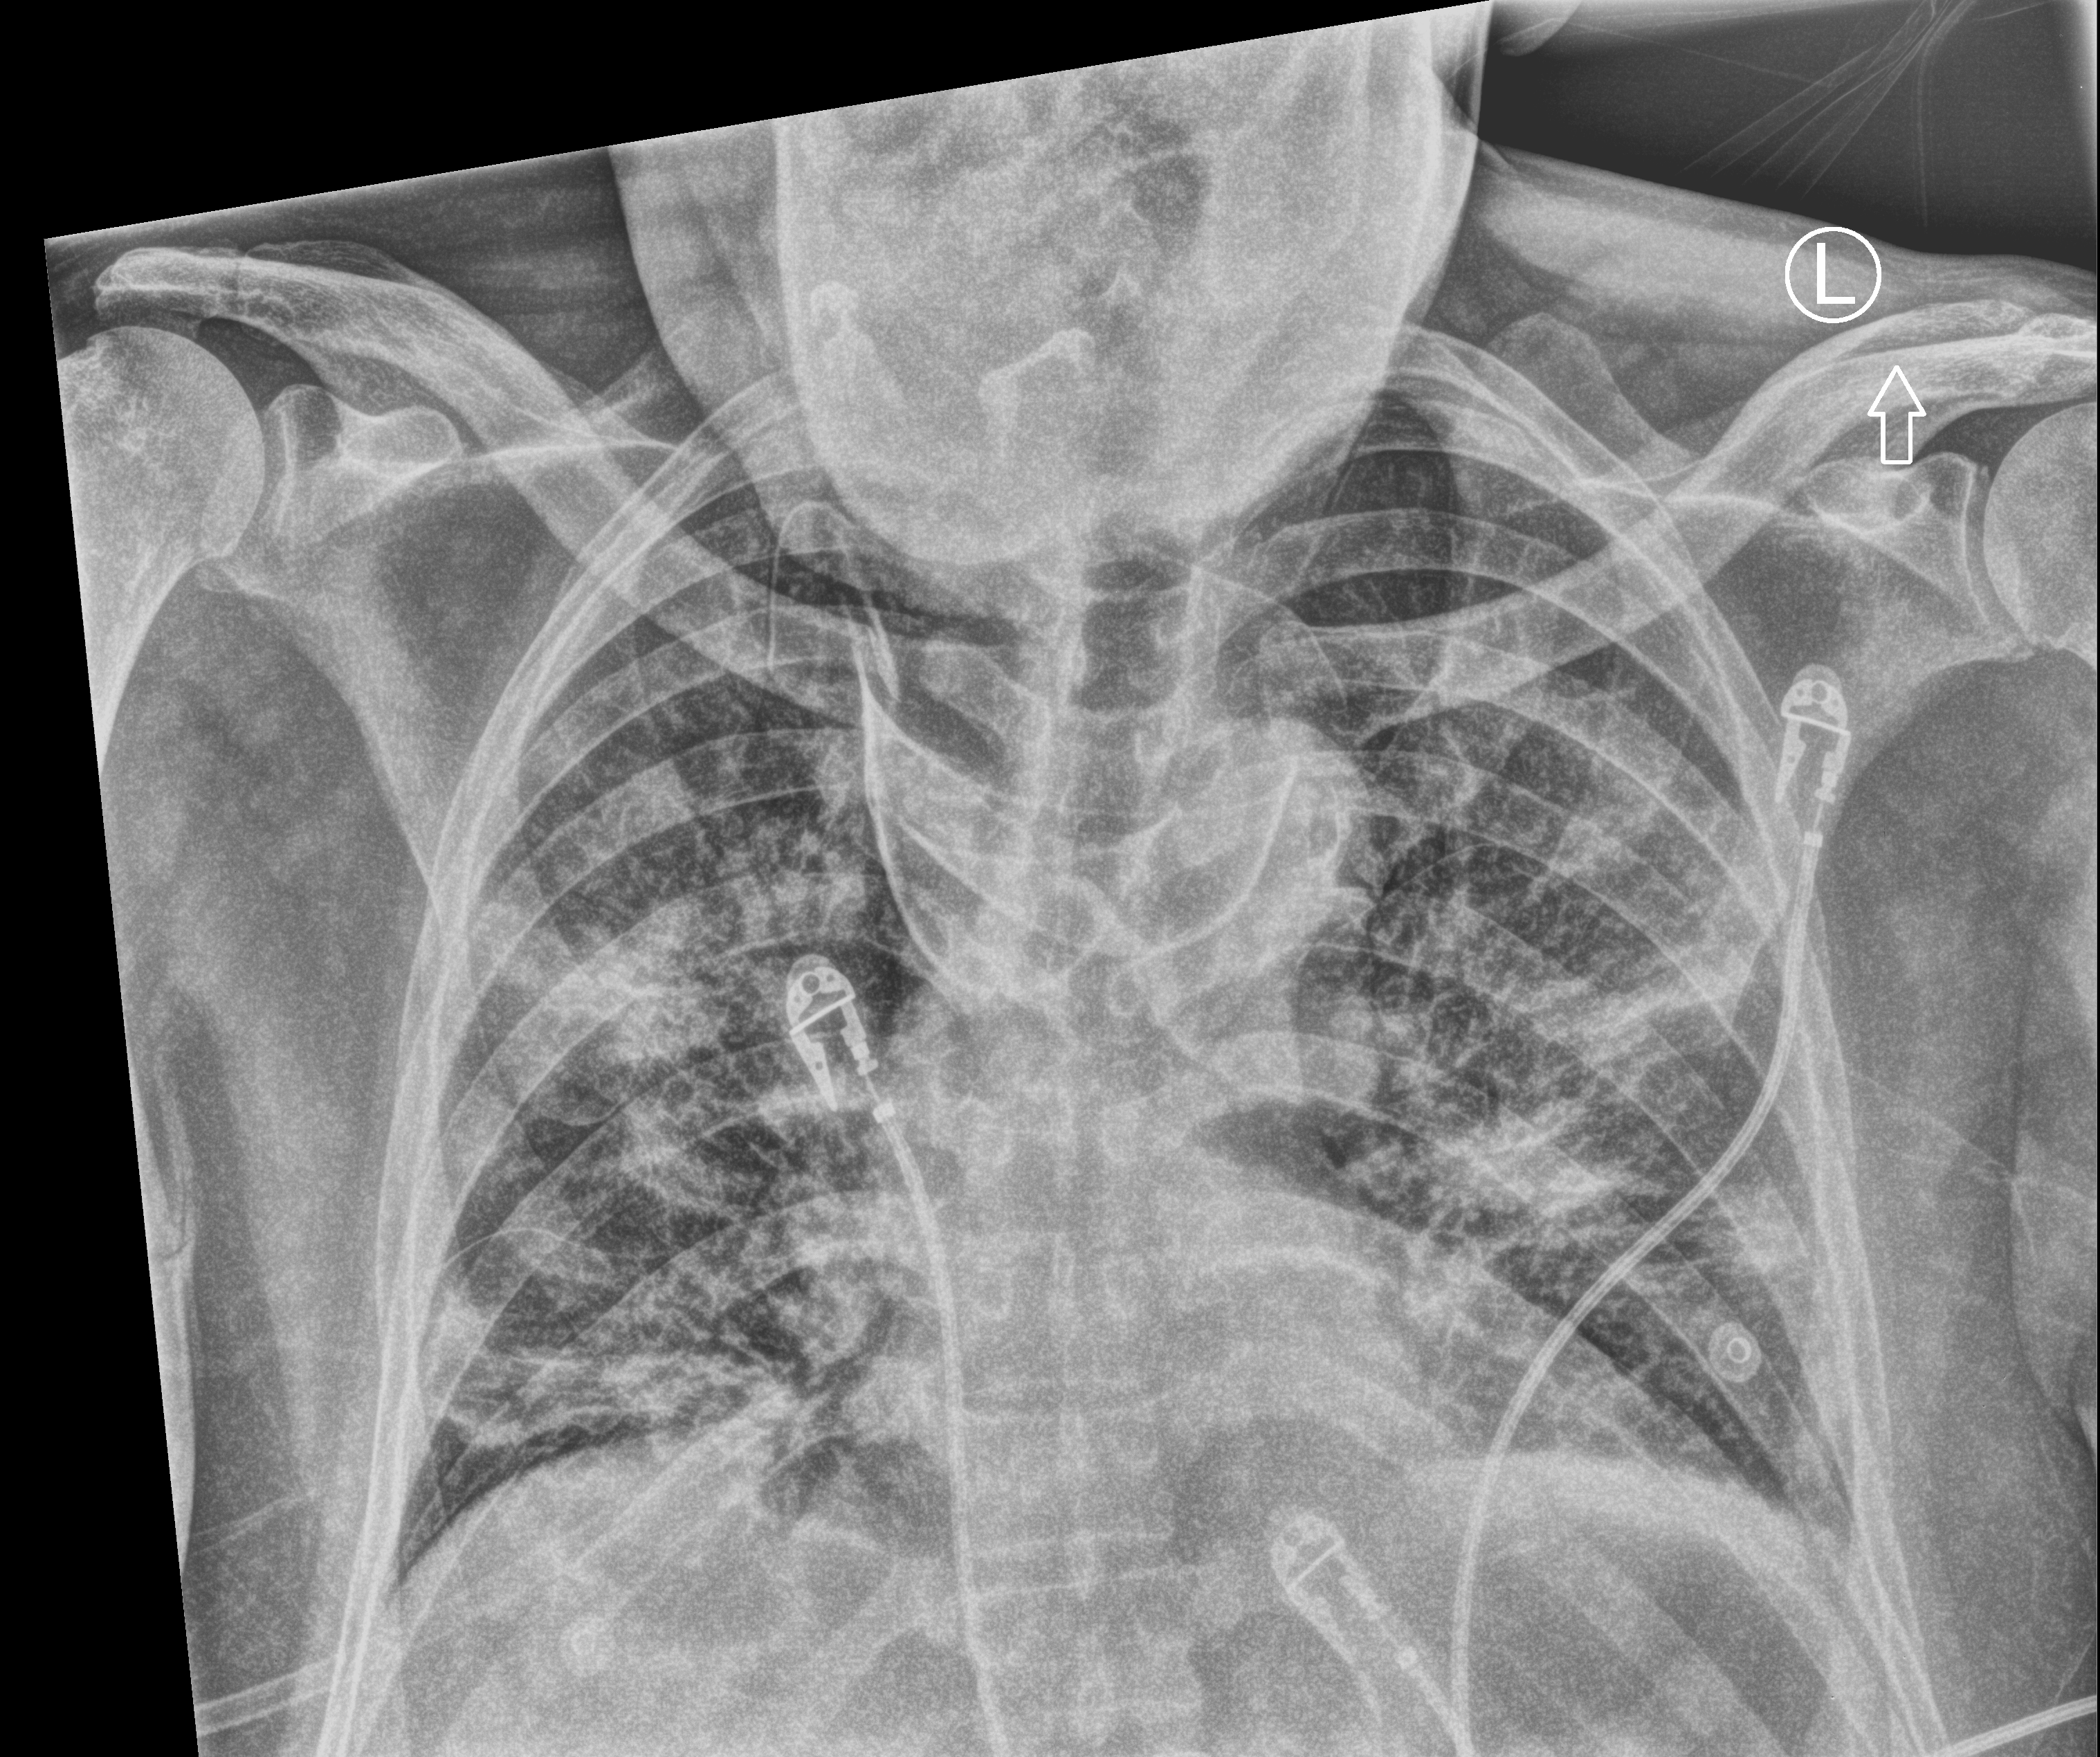
Chest X-ray (portable), anteroposterior (AP) projection. Male patient hospitalised with COVID-19, age 60–74 years.
Admission-level facts for this patient (not findings on this image; timing relative to this image not recorded): mechanically ventilated during this hospital stay: no; admitted to intensive care during this hospital stay: no.